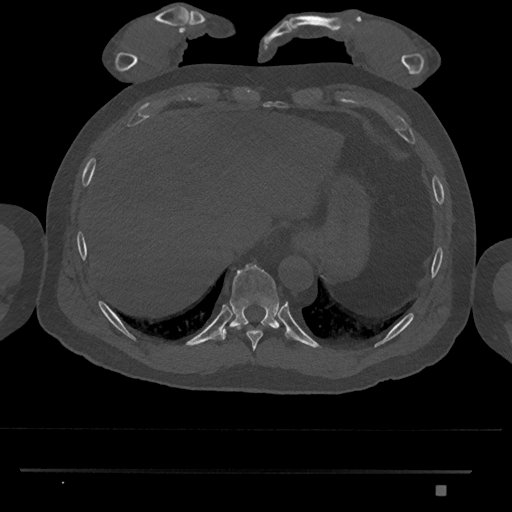
CT including the spine, one axial slice; position 1024 of 1134 along the scan axis; 120 kVp; bone window (W 1800 / L 400 HU); 0.5 mm slice thickness; 512 × 512 image matrix, field of view 429 × 429 mm. Male patient, age 65 years. Case-level facts recorded for this patient, not image findings: primary cancer: prostate.
Outlined on this slice (semi-automatic segmentation, software-assisted and operator-edited):
- T10 vertebra: bounding box [x1, y1, x2, y2] px = [220, 264, 279, 340]
- T9 vertebra: [235, 325, 273, 351]